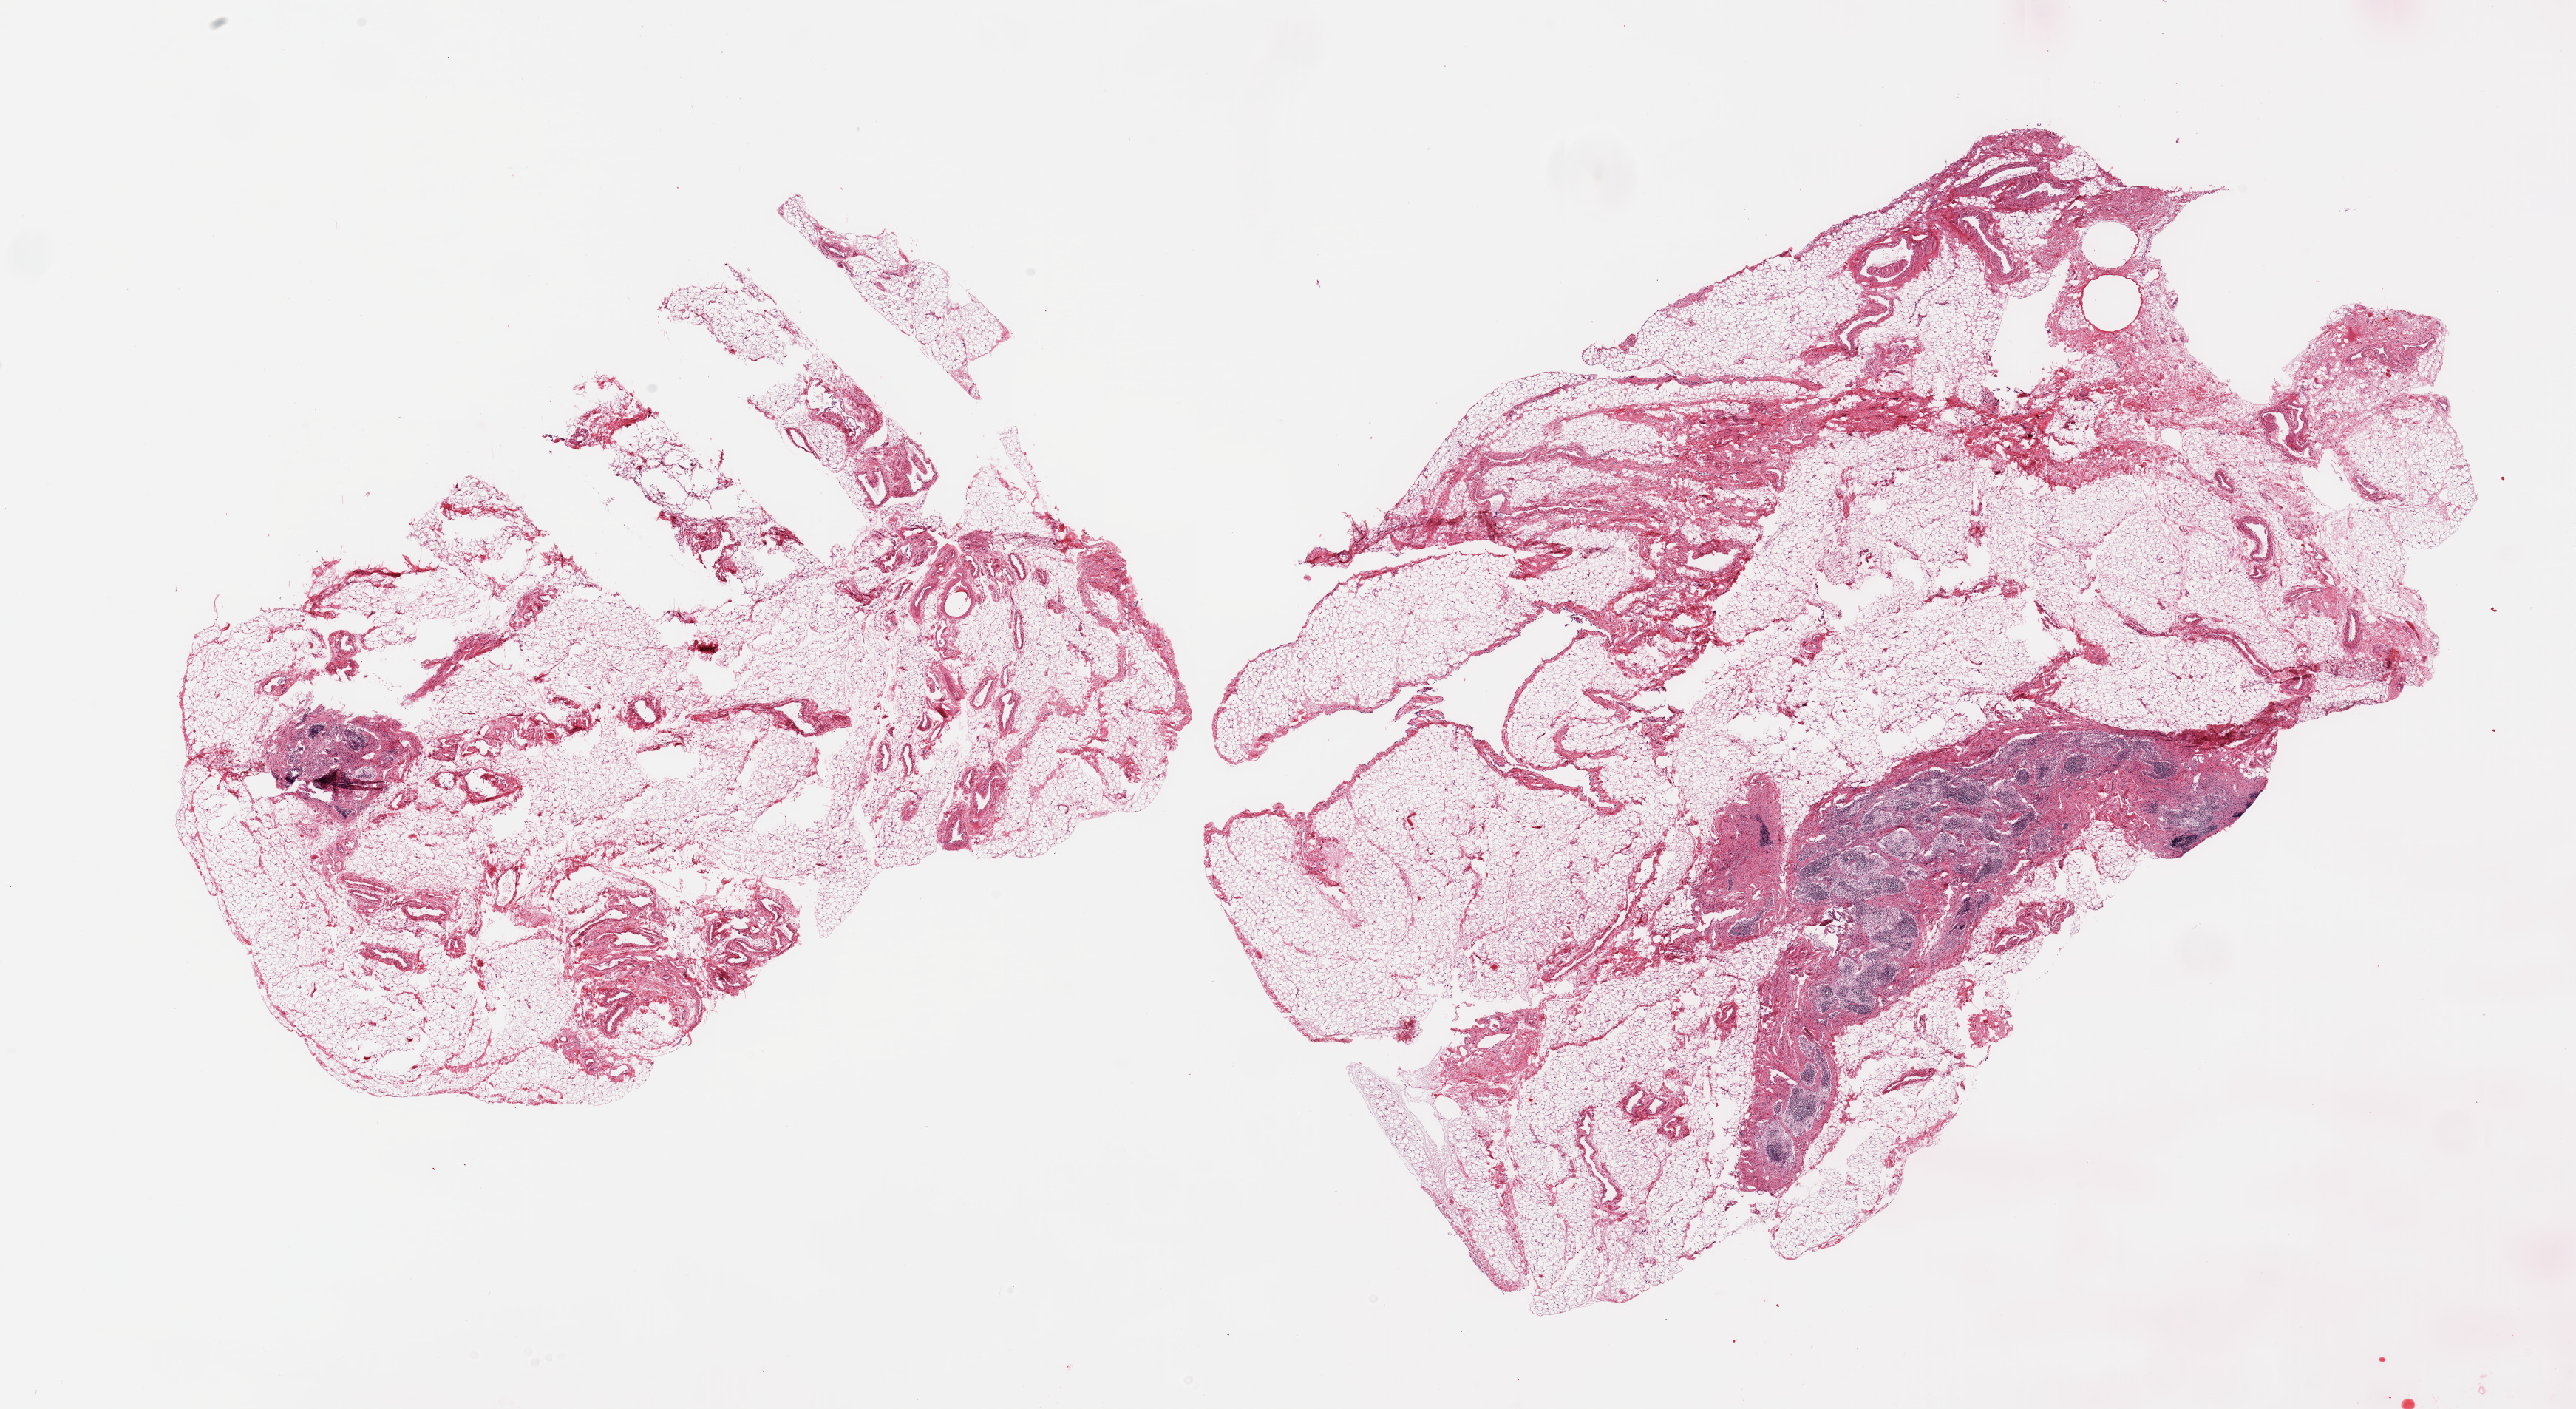
Whole-slide image, hematoxylin and eosin (H&E) stain, brightfield — low-resolution overview of the scanned area, about 27.6 x 15.1 mm, PAXgene-fixed paraffin-embedded (PFPE) section, target tissue: omentum, donor tissue sample. Female donor.
Reviewer comment on this tissue sample: 2 pieces; portions of lymph nodes in each piece: 1 occupies 20%, other 5% of sample.